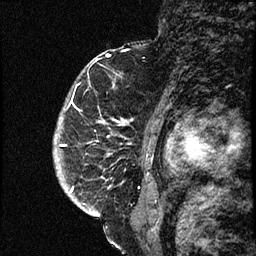
Breast MRI (dynamic contrast-enhanced), one sagittal slice; position 53 of 66 along the scan axis; dynamic contrast-enhanced study with each time point stored as its own series, time point 2 of 3 at this slice position (early post-contrast, ordered by acquisition time); 1.5 T; TE 4.2 ms, TR 17.6 ms; 256 × 256 image matrix, field of view 200 × 200 mm. Female patient. Case-level facts recorded for this patient, not image findings: setting: breast cancer imaged before/during neoadjuvant chemotherapy; receptor status: HER2-positive.
Annotated regions visible in this slice (semi-automatically segmented with operator editing):
- analysis volume of interest (the breast-tissue region the enhancement analysis was run in; not a lesion): bounding box <54,69,139,209> (left, top, right, bottom; pixels)
- tumour enhancement mask (voxels above the 100 % enhancement threshold inside the analysis volume of interest): <57,118,128,206>